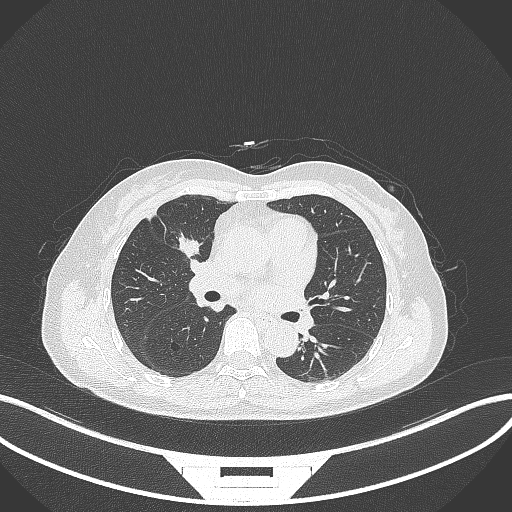
Chest CT, one axial slice. Slice 164 of 284 in the series (ordered by position). Reconstruction kernel B70f. 120 kVp. Lung window (W 1500 / L -600 HU). 1 mm slice thickness. 512 × 512 image matrix, field of view 400 × 400 mm. Patient: female, 51 years. From the clinical record (not read from this slice): clinical TNM (as recorded): T1c N0 M0; histopathological grade: G2.
Structures marked on this image (bounding box drawn by a radiologist):
- lung tumour (recorded histology: adenocarcinoma): bounding box (x1, y1, x2, y2) in pixels: (176, 228, 205, 263)